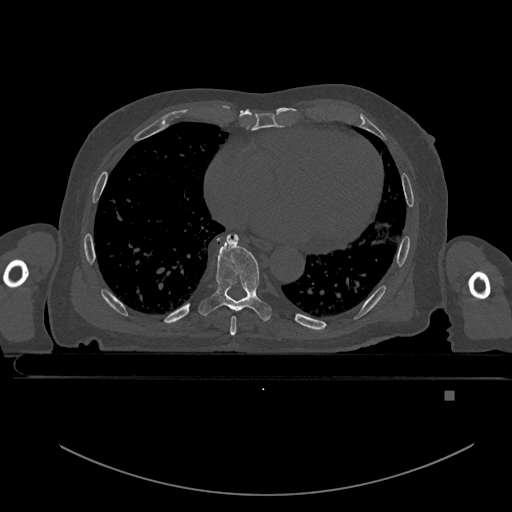
CT including the spine, one axial slice. Slice 208 of 969 in the series (ordered by position). Bone window (W 1800 / L 400 HU). 0.5 mm slice thickness. 512 × 512 image matrix, field of view 456 × 456 mm. Patient: male, 82 years. From the clinical record (not read from this slice): primary cancer: prostate; vertebrae with lytic lesions (as recorded): T11, T9, T8, T2.
Outlined on this slice (semi-automatically segmented with operator editing):
- T7 vertebra: box from (x=230, y=316) to (x=236, y=335) px
- T8 vertebra: (x=198, y=234)–(x=272, y=321)